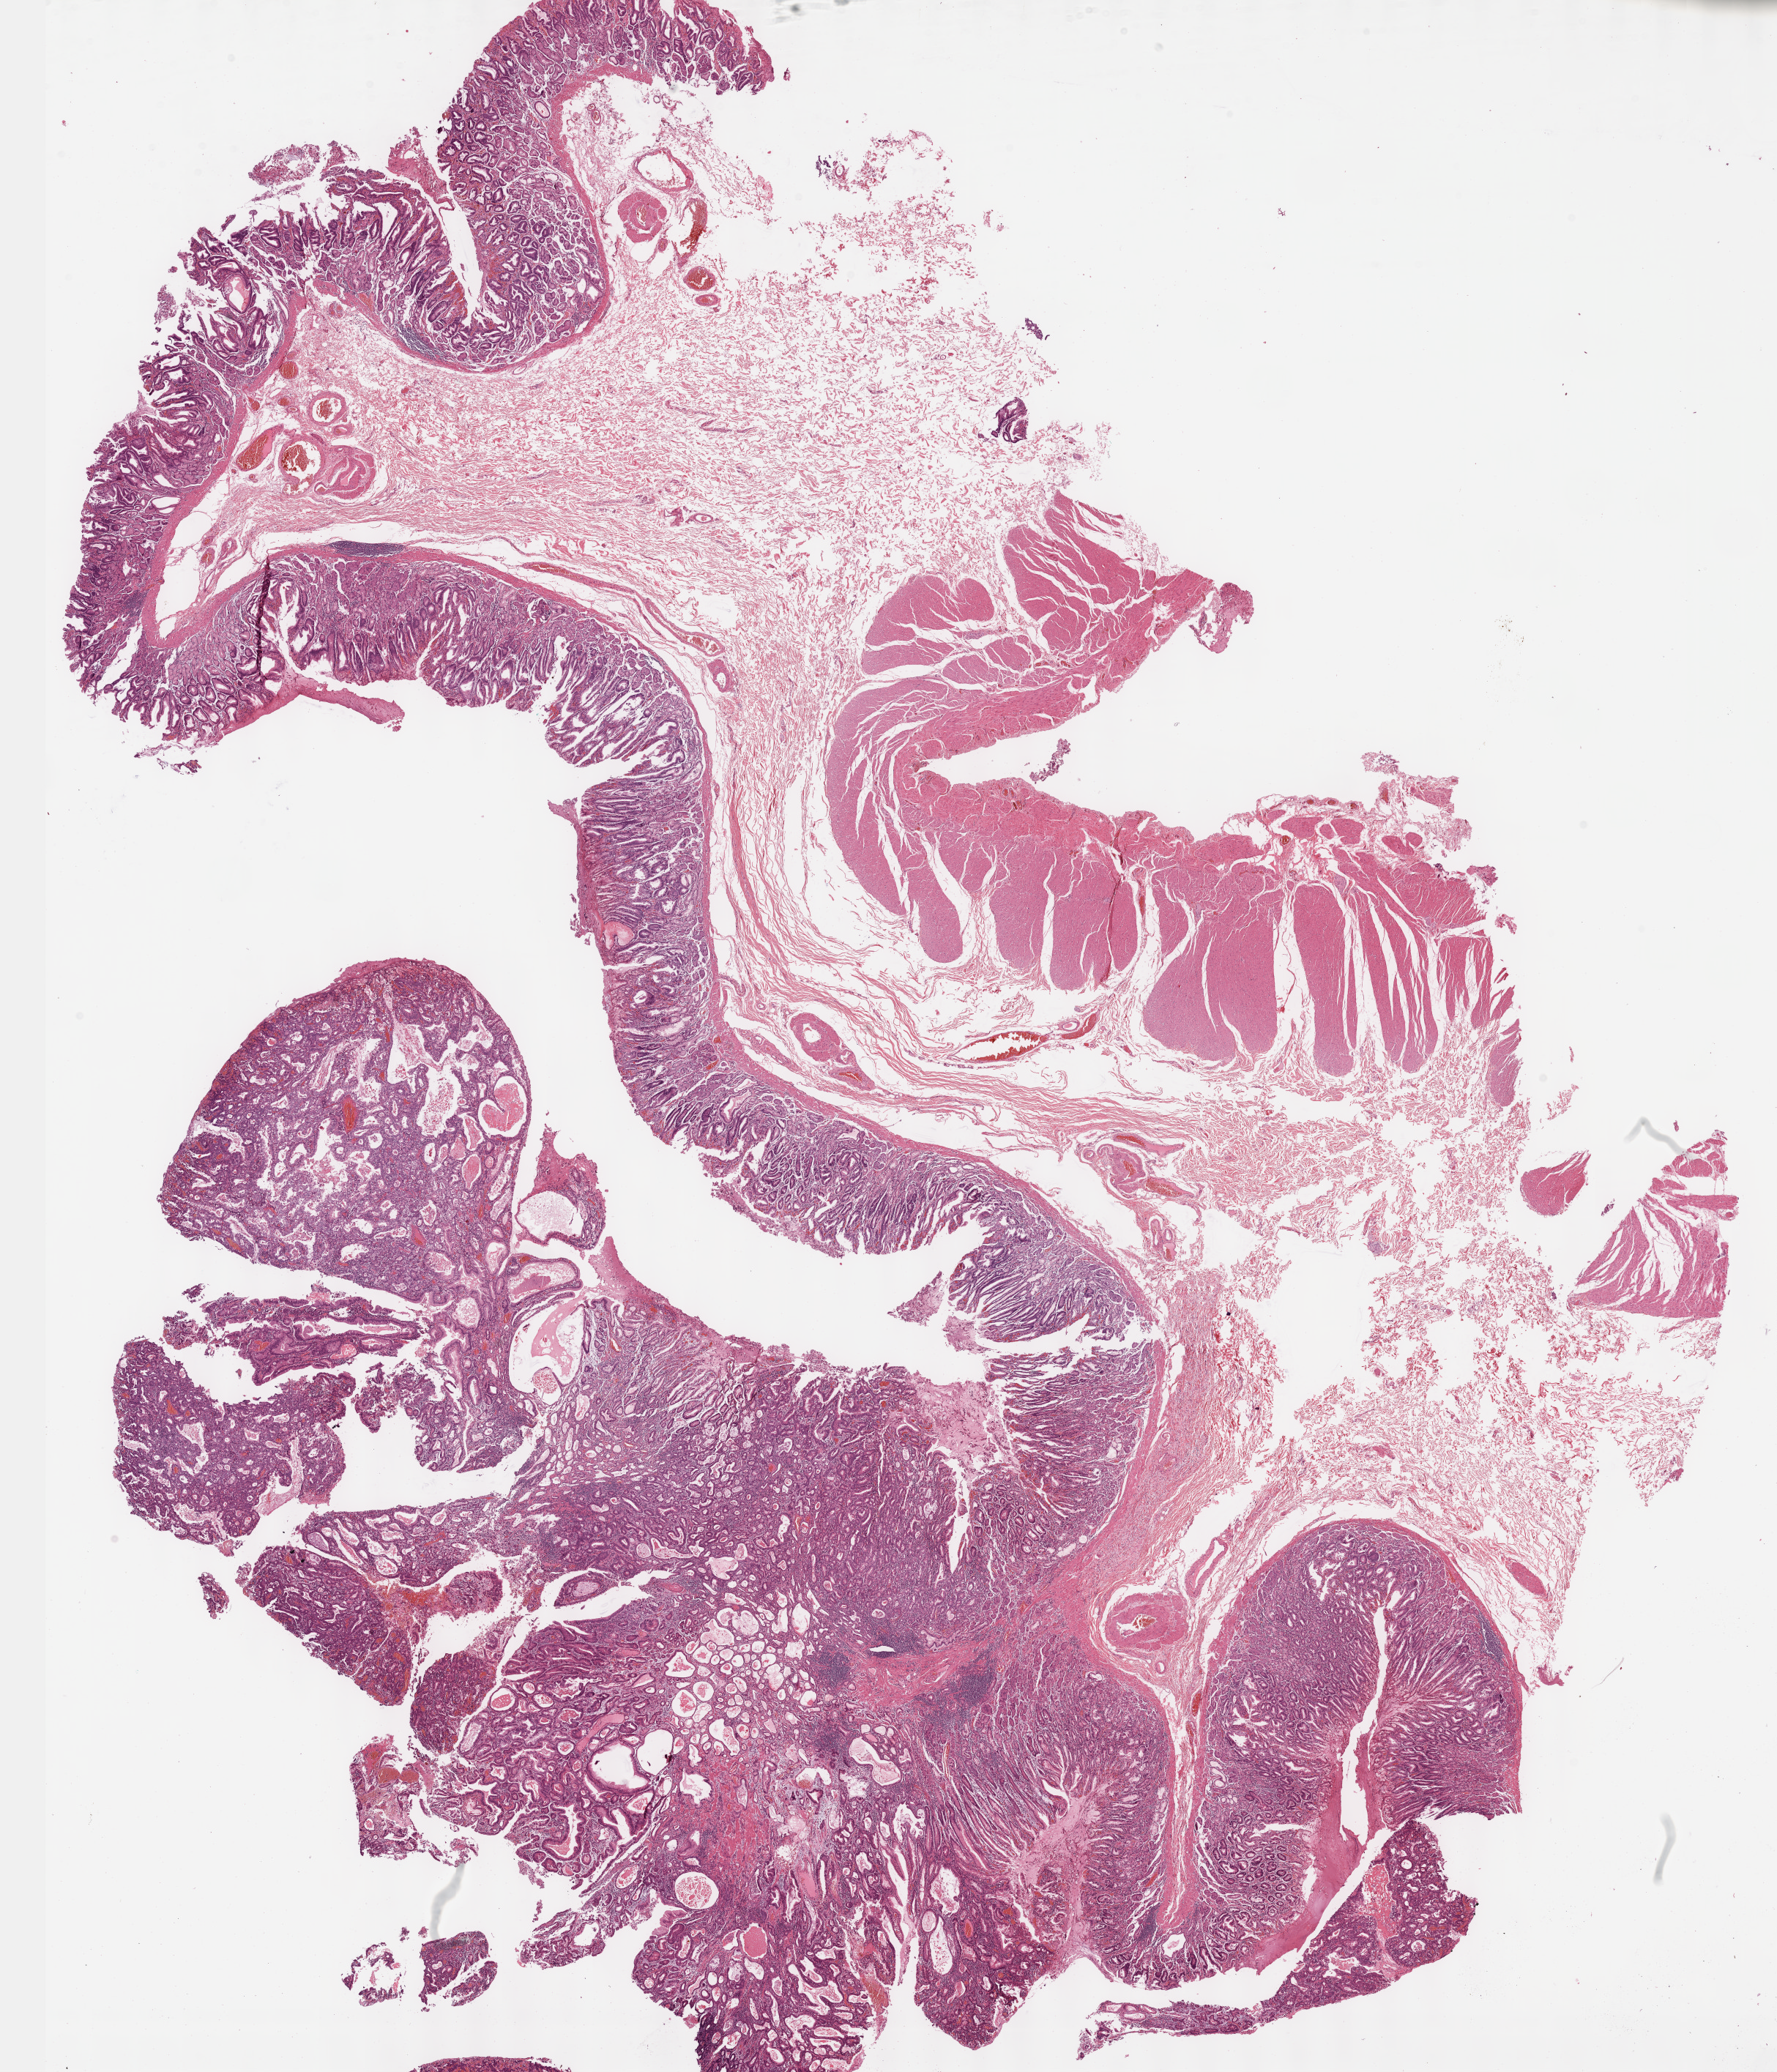
Digitized Hematoxylin and eosin (H&E) stained tissue section (whole slide) — low-resolution overview of the scanned area, about 19.6 x 22.9 mm (from a 40x scan), FFPE section, primary tumour sample from the stomach. Male, age 51 years at initial diagnosis. Histologic grade: G2 (moderately differentiated).
Histologic diagnosis: Adenocarcinoma, intestinal type. AJCC pathologic stage: IA (6th edition).